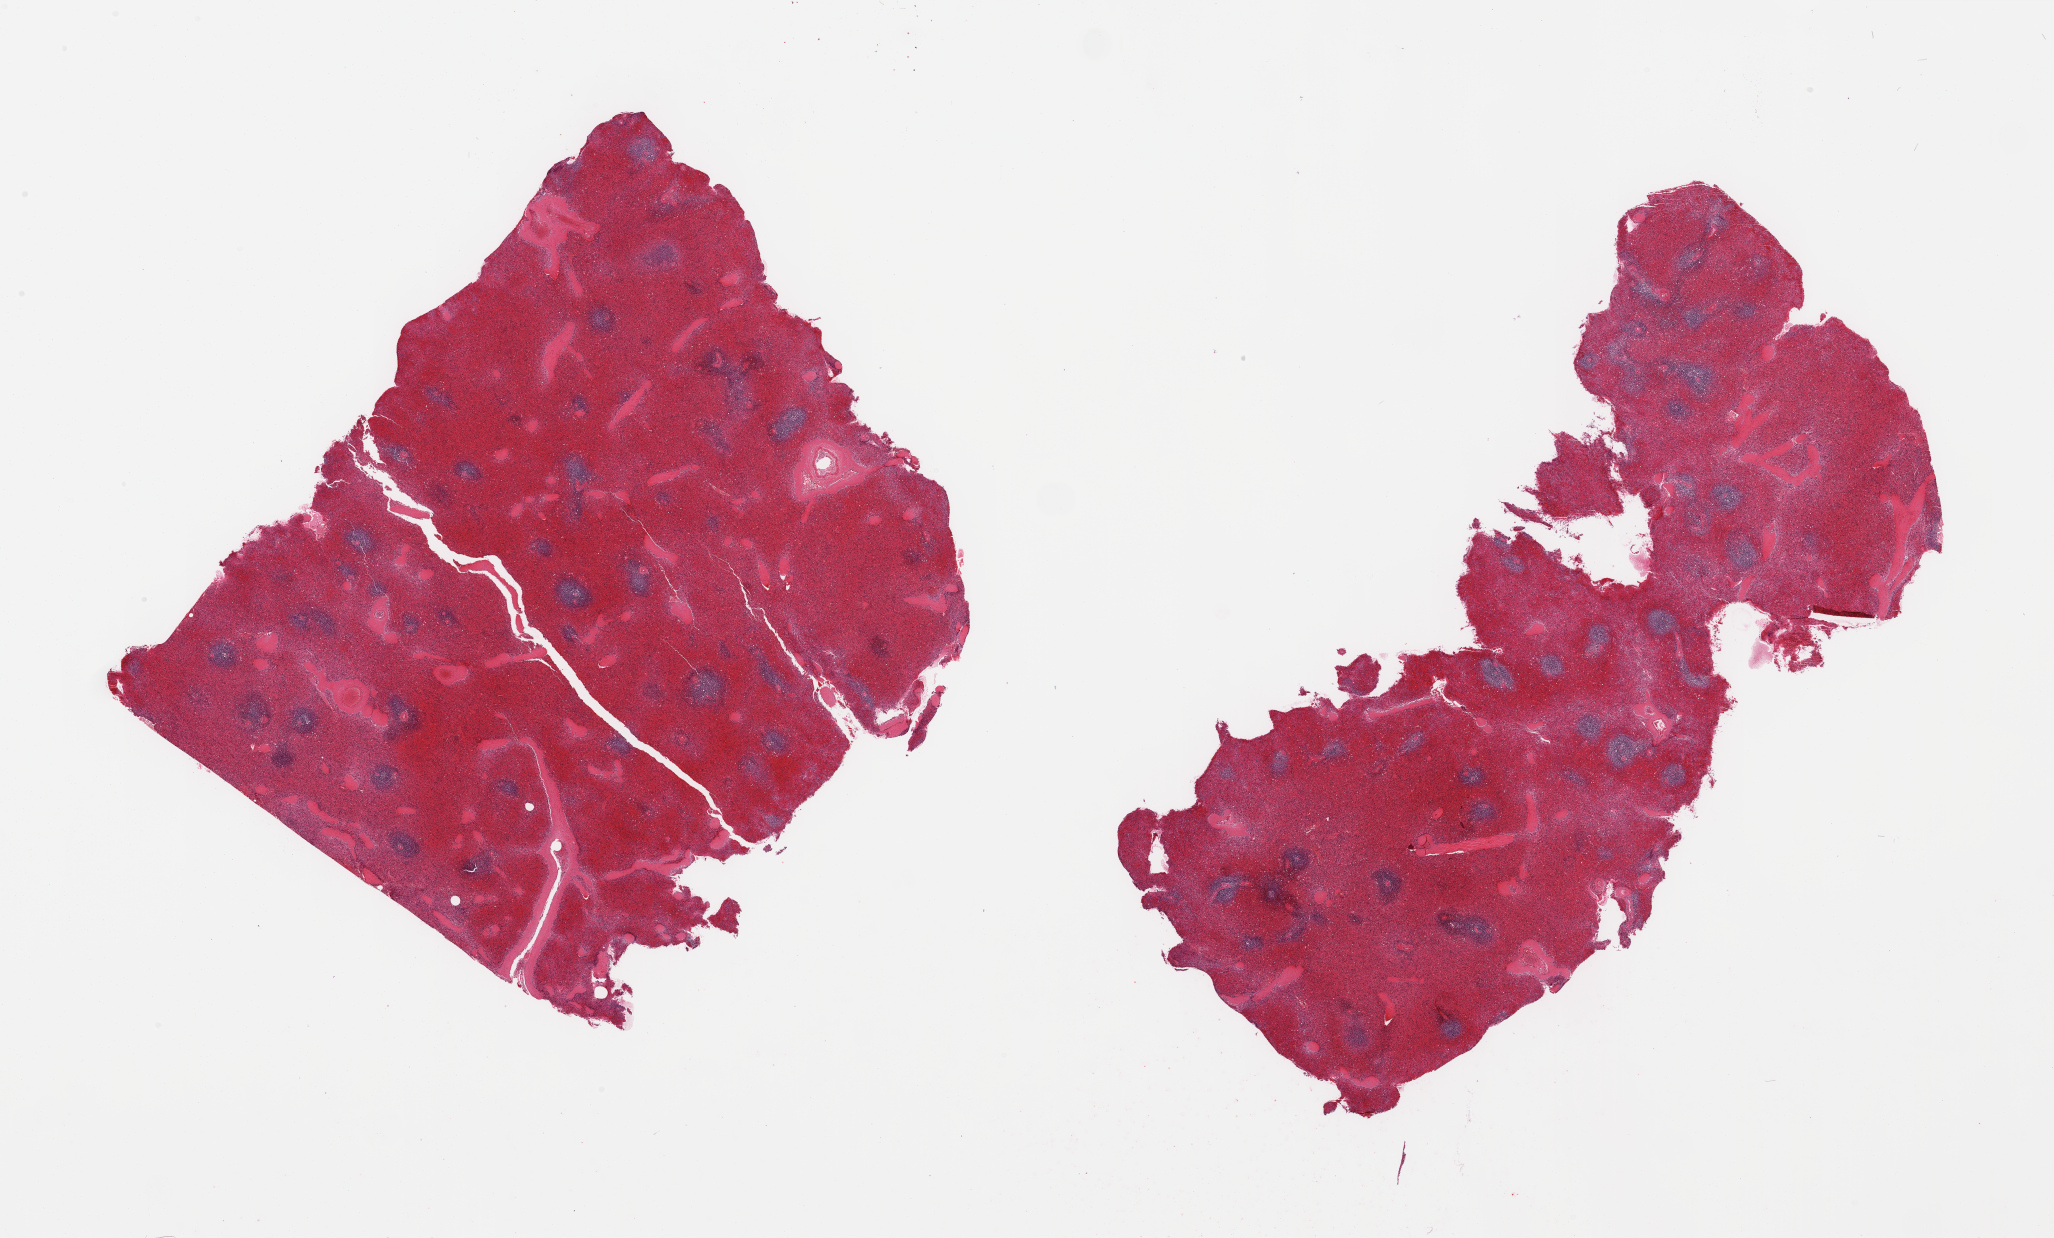
Whole-slide image, hematoxylin and eosin (H&E) stain — whole scanned area (about 32.5 x 19.6 mm, acquisition: 20x scan) shown as a low-resolution overview. PAXgene-fixed paraffin-embedded (PFPE) section. Target tissue: spleen. Tissue donor sample.
* review note (as recorded): 2 pieces; moderate red pulp congestion